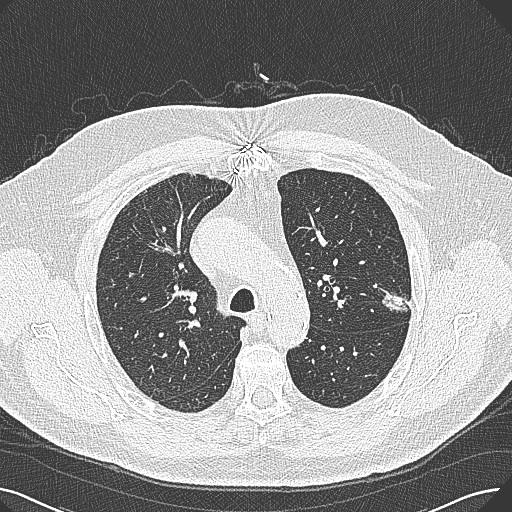
Axial slice from a low-dose chest CT screening exam. Baseline screening round. Lung window (W 1500 / L -600 HU). Lung (sharp) reconstruction kernel (B80f). 120 kVp. 512 × 512 image matrix, field of view 370 × 370 mm. Male, age 74 years at enrolment.
Expert-annotated lung lesion, bounding box (x1, y1, x2, y2) in pixels: (372, 273, 425, 320). Screening reader's record for this exam (one nodule recorded; not confirmed to be the boxed lesion): non-calcified nodule or mass ≥4 mm, left upper lobe, 15 × 10 mm, poorly defined margins, soft tissue attenuation. Official screen result: positive, change unspecified: nodule(s) >= 4 mm or enlarging nodule(s), mass(es), or other non-specific abnormalities suspicious for lung cancer. Participant outcome: lung cancer diagnosed 124 days after this screen — adenocarcinoma, NOS, left upper lobe, well differentiated (G1), stage IA (AJCC 6th edition), 26 mm at pathology.